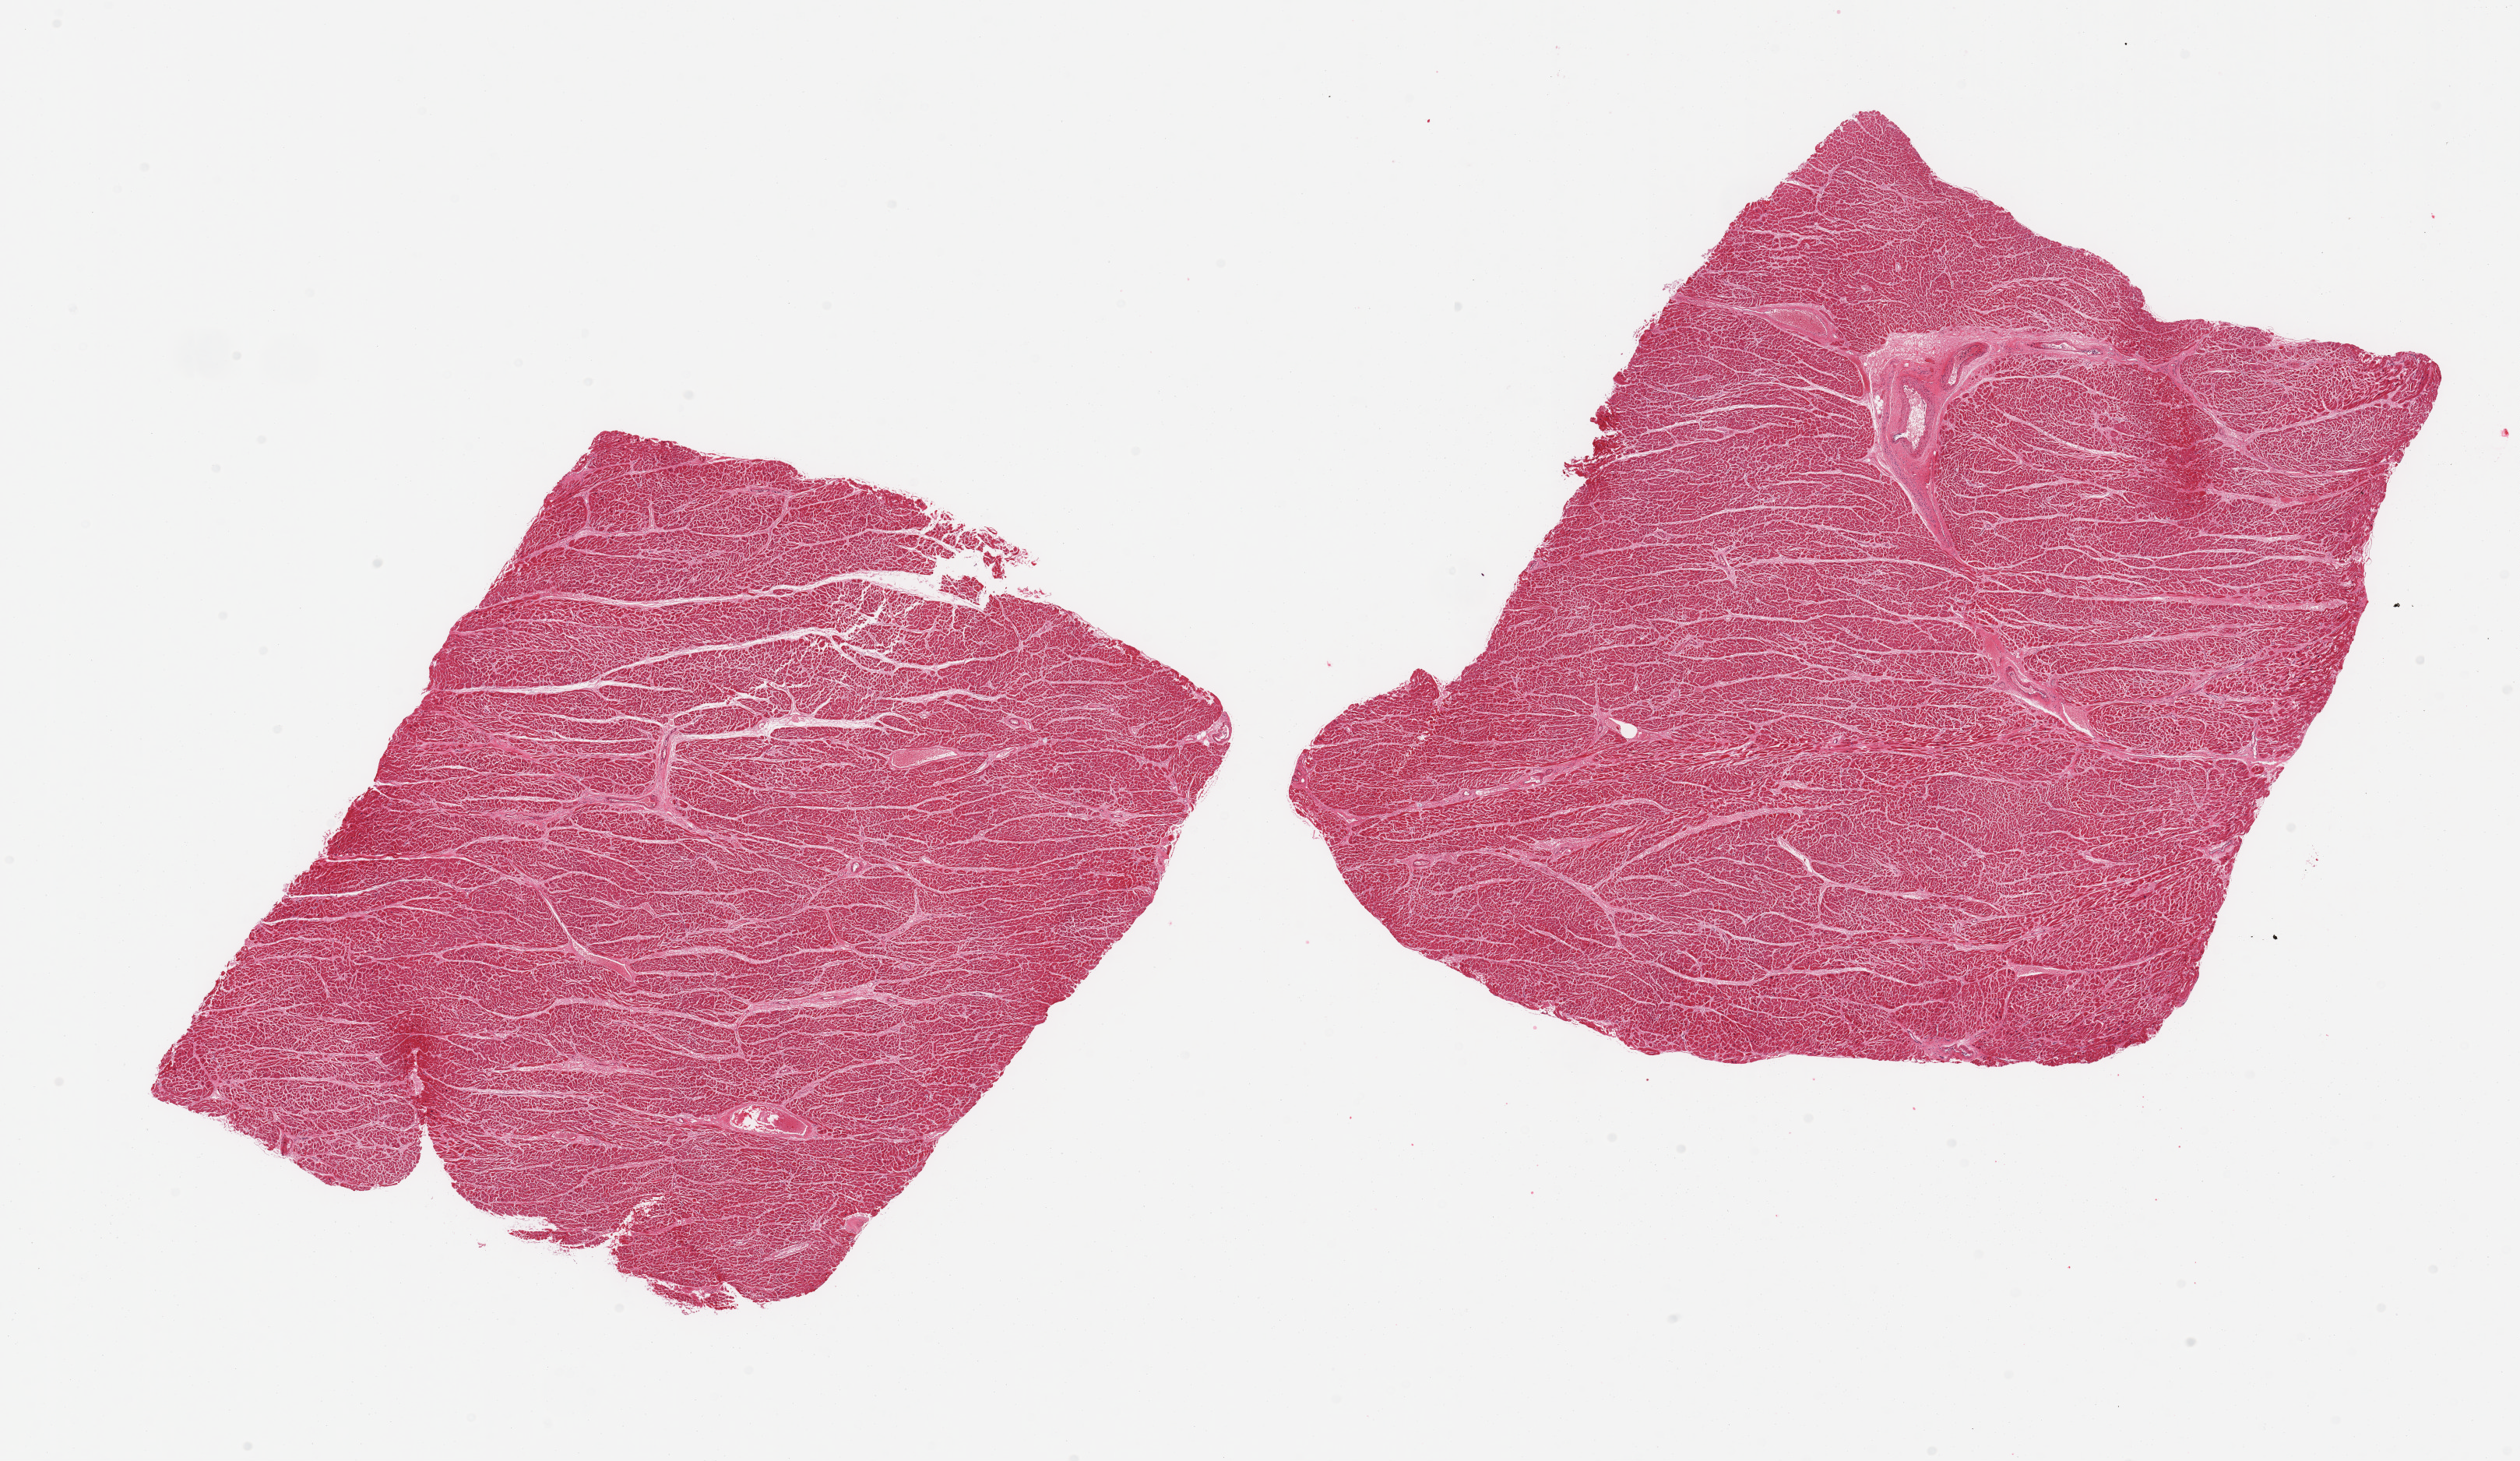
Whole-slide image, haematoxylin and eosin stain, brightfield, a low-resolution overview of the entire scanned area, about 25.6 x 14.8 mm (slide scanned at 20x), PAXgene-fixed paraffin-embedded (PFPE) section, section of heart (target tissue), tissue donor sample. Donor: male.
Reviewer comment on this tissue sample: 2 pieces, moderate interstitial fibrosis/chronic ischemic changes.